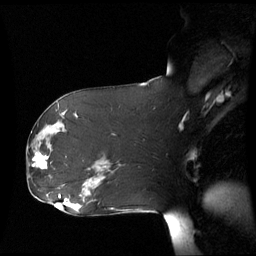
Breast MRI (dynamic contrast-enhanced), one sagittal slice. Slice 33 of 60 in the series (ordered by position). Dynamic contrast-enhanced series, image 2 of 3 at this slice position (ordered by acquisition). 1.5 T. TE 4.2 ms, TR 8.9 ms. 256 × 256 image matrix, field of view 280 × 280 mm. Female patient, age 61 years. From the clinical record (not read from this slice): setting: breast cancer imaged before/during neoadjuvant chemotherapy; receptor status: HR-positive, HER2-negative.
Structures marked on this image (semi-automatic segmentation, software-assisted and operator-edited):
- analysis volume of interest (the breast-tissue region the enhancement analysis was run in; not a lesion): box from (x=26, y=142) to (x=53, y=177) px
- tumour enhancement mask (voxels above the 70 % enhancement threshold inside the analysis volume of interest): (x=34, y=154)–(x=49, y=169)